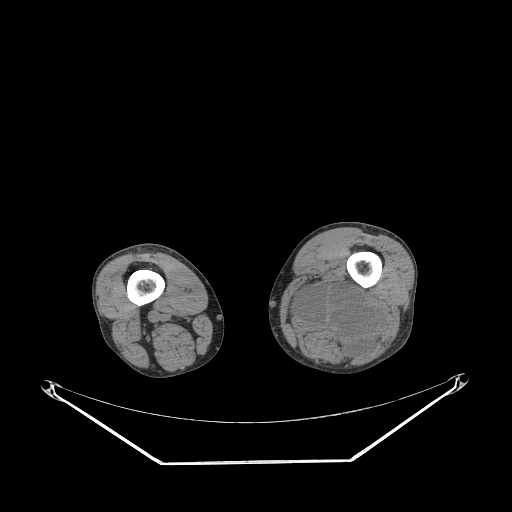
CT of an extremity soft-tissue mass (from a PET/CT study), one axial slice; slice 210 of 267 in the series (ordered by position); reconstruction kernel STANDARD; 140 kVp; soft-tissue window (W 400 / L 40 HU); 3.75 mm slice thickness; 512 × 512 image matrix. Male patient. From the clinical record (not read from this slice): histological type: undifferentiated pleomorphic liposarcoma; grade: high; site of the primary tumour: left thigh.
Outlined on this slice (expert contour drawn on MRI and transferred to this co-registered scan by the dataset authors):
- gross tumour volume including surrounding oedema: bounding box [x1, y1, x2, y2] px = [290, 274, 378, 357]
- gross tumour volume (mass): [299, 290, 371, 343]